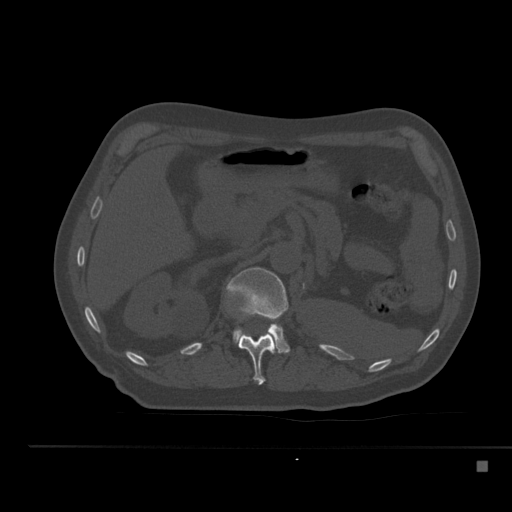
CT including the spine, one axial slice. Slice 220 of 517 in the series (ordered by position). Reconstruction kernel Br40s. 120 kVp. Bone window (W 1800 / L 400 HU). 1.5 mm slice thickness. 512 × 512 image matrix, field of view 408 × 408 mm. Male patient, age 70 years. From the clinical record (not read from this slice): primary cancer: renal.
Outlined on this slice (semi-automatic segmentation, software-assisted and operator-edited):
- L1 vertebra: bounding box (x1, y1, x2, y2) in pixels: (226, 267, 290, 353)
- T12 vertebra: (238, 317, 275, 385)